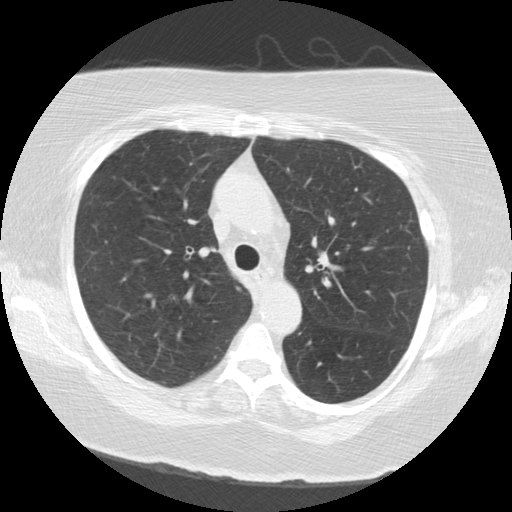
Axial slice from a low-dose chest CT screening exam. First (baseline) screen. Lung window (W 1500 / L -600 HU). Standard (soft-tissue) reconstruction kernel (STANDARD). 120 kVp. 512 × 512 image matrix. Female, age 64 years at enrolment. Current smoker at enrolment.
Expert reader's lesion annotation, box from (x=150, y=169) to (x=179, y=194) px. No non-calcified nodule or mass ≥4 mm was recorded by the screening reader at this exam.